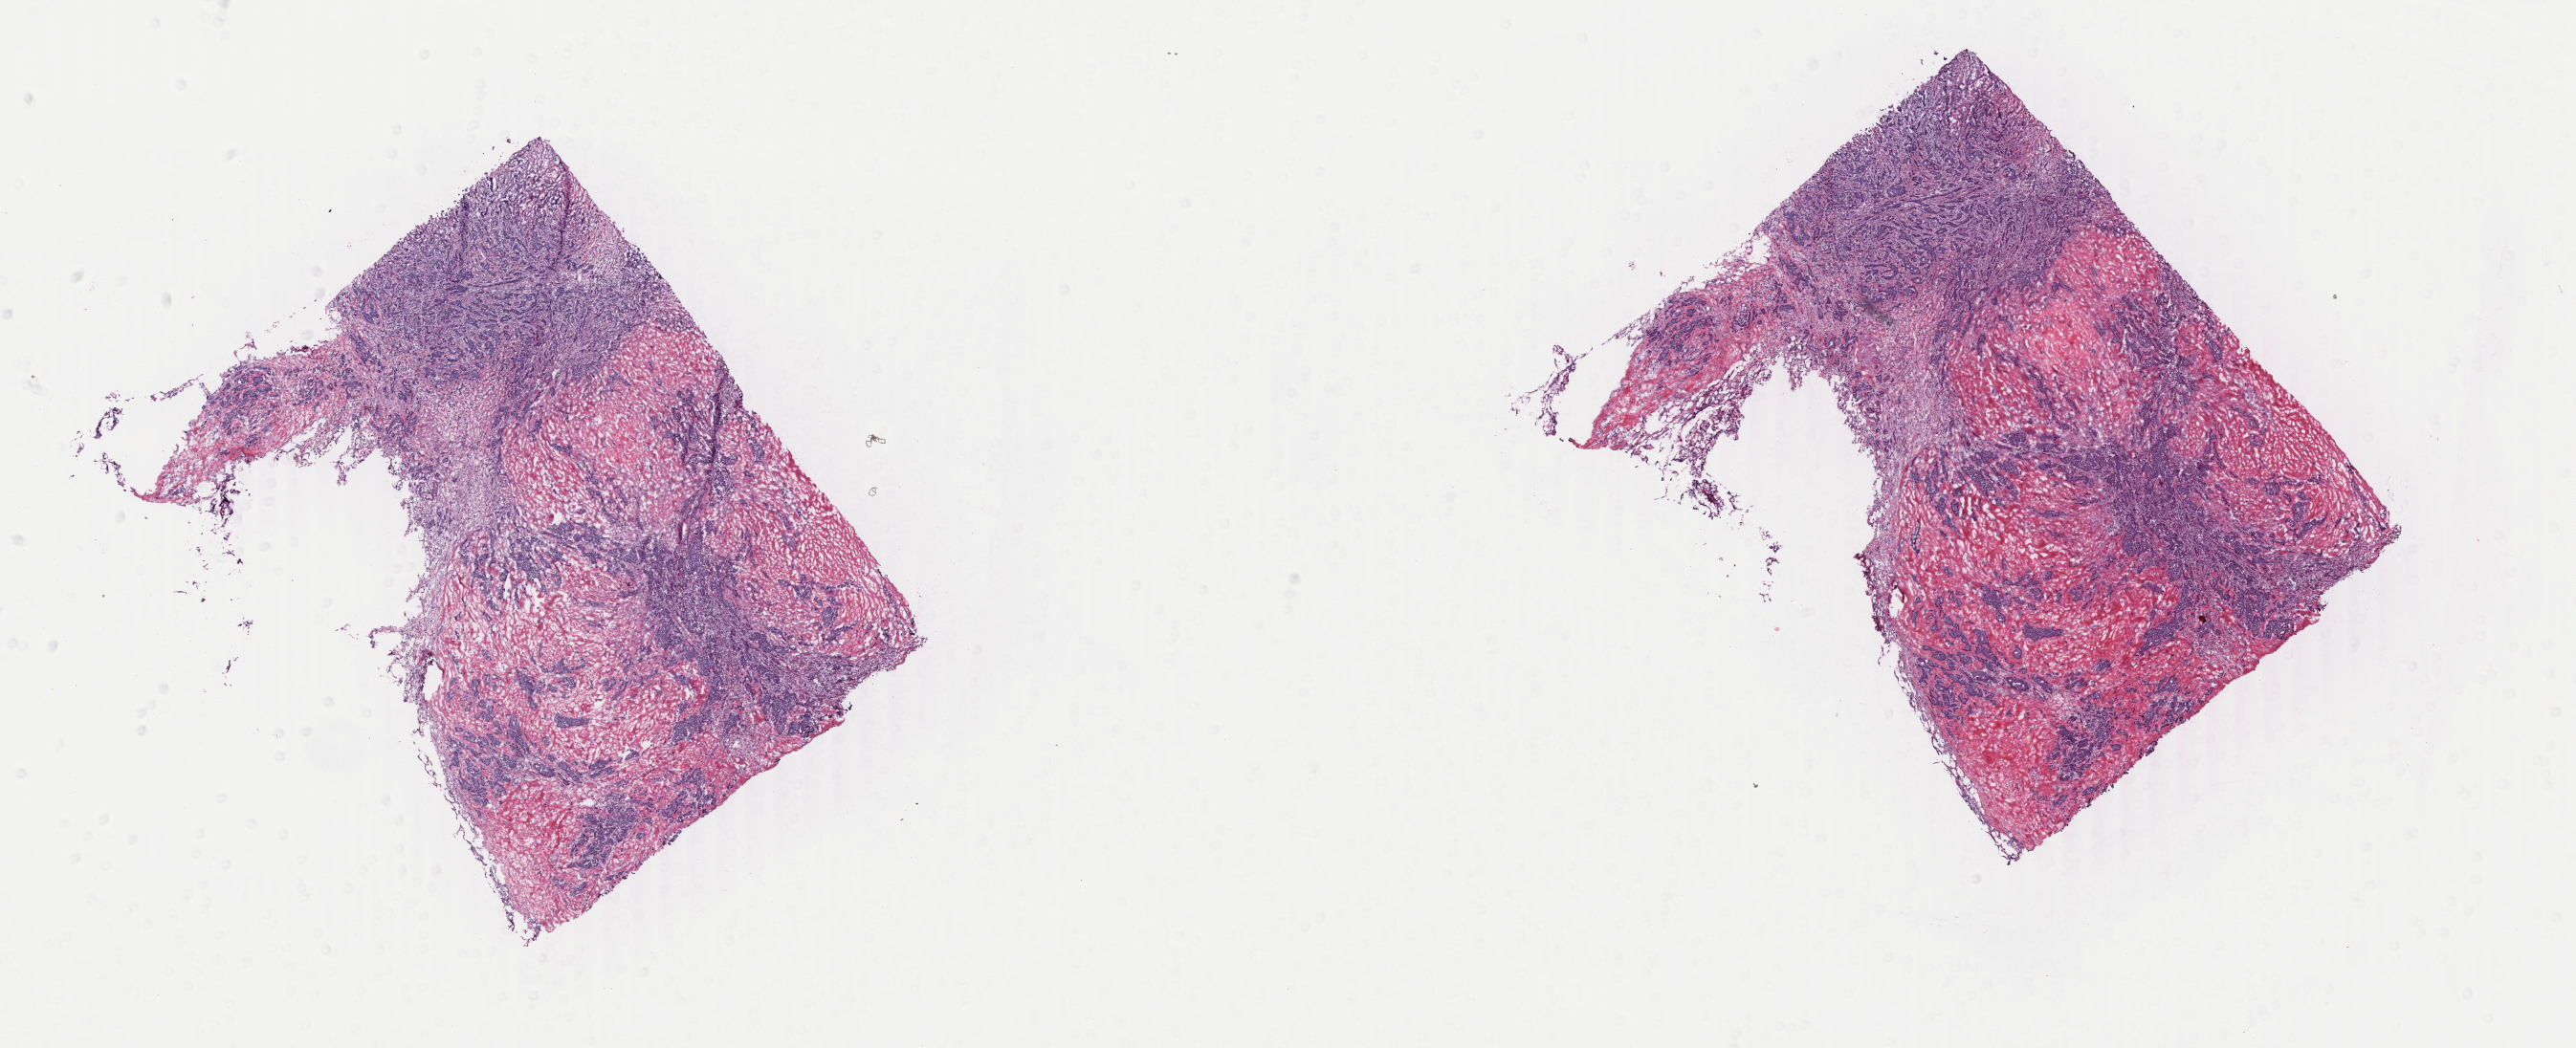
H&E-stained whole-slide image — low-resolution overview of the scanned area, about 21.4 x 8.7 mm (from a 40x scan). Frozen section. Primary tumour sample from the breast. Female patient; age at initial diagnosis 80 years. Pathologist review of this section (percent, as recorded): tumour cells 70%, tumour nuclei 75%, normal cells 0%, stromal cells 30%, necrosis 0%. Infiltration values recorded for this section: lymphocyte infiltration 5%, monocyte infiltration 0%, neutrophil infiltration 0%.
Lymph nodes positive (case pathology): 0 of 6 examined. Laterality: left. Diagnosis: Infiltrating duct carcinoma, NOS. AJCC pathologic stage: IA (6th edition).